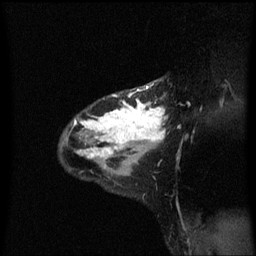
Breast MRI (dynamic contrast-enhanced), one sagittal slice; slice 42 of 60 in the series (ordered by position); dynamic contrast-enhanced series, image 2 of 3 at this slice position (ordered by acquisition); 1.5 T; TE 4.2 ms, TR 8.4 ms; 256 × 256 image matrix. Female patient, age 32 years.
Structures marked on this image (semi-automatic segmentation, software-assisted and operator-edited):
- analysis volume of interest (the breast-tissue region the enhancement analysis was run in; not a lesion): bounding box (x1, y1, x2, y2) in pixels: (61, 80, 169, 167)
- tumour enhancement mask (voxels above the 70 % enhancement threshold inside the analysis volume of interest): (68, 86, 167, 159)